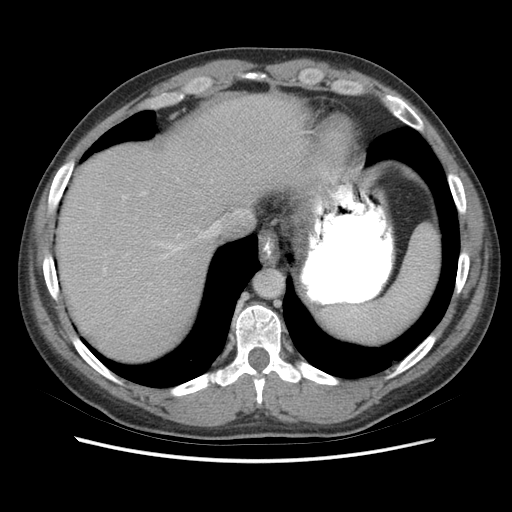
Contrast-enhanced abdominal CT (liver protocol), one axial slice; soft-tissue window (W 400 / L 40 HU); 2.5 mm slice thickness; 512 × 512 image matrix, field of view 360 × 360 mm. From the clinical record (not read from this slice): diagnosis: hepatocellular carcinoma (patient treated with transarterial chemoembolisation; whether this scan precedes or follows treatment is not stated here); TNM stage (as recorded): Stage-IIIA; Child-Pugh class: A; tumour nodularity: multinodular; tumour size: 6.6 cm.
Outlined on this slice (semi-automatically segmented with operator editing):
- abdominal aorta: box from (x=255, y=270) to (x=283, y=297) px
- liver parenchyma outside the tumour (the mass and vessels are separate outlines, so this box may not span the whole liver): (x=56, y=94)–(x=318, y=360)
- liver vessels: (x=104, y=225)–(x=218, y=271)